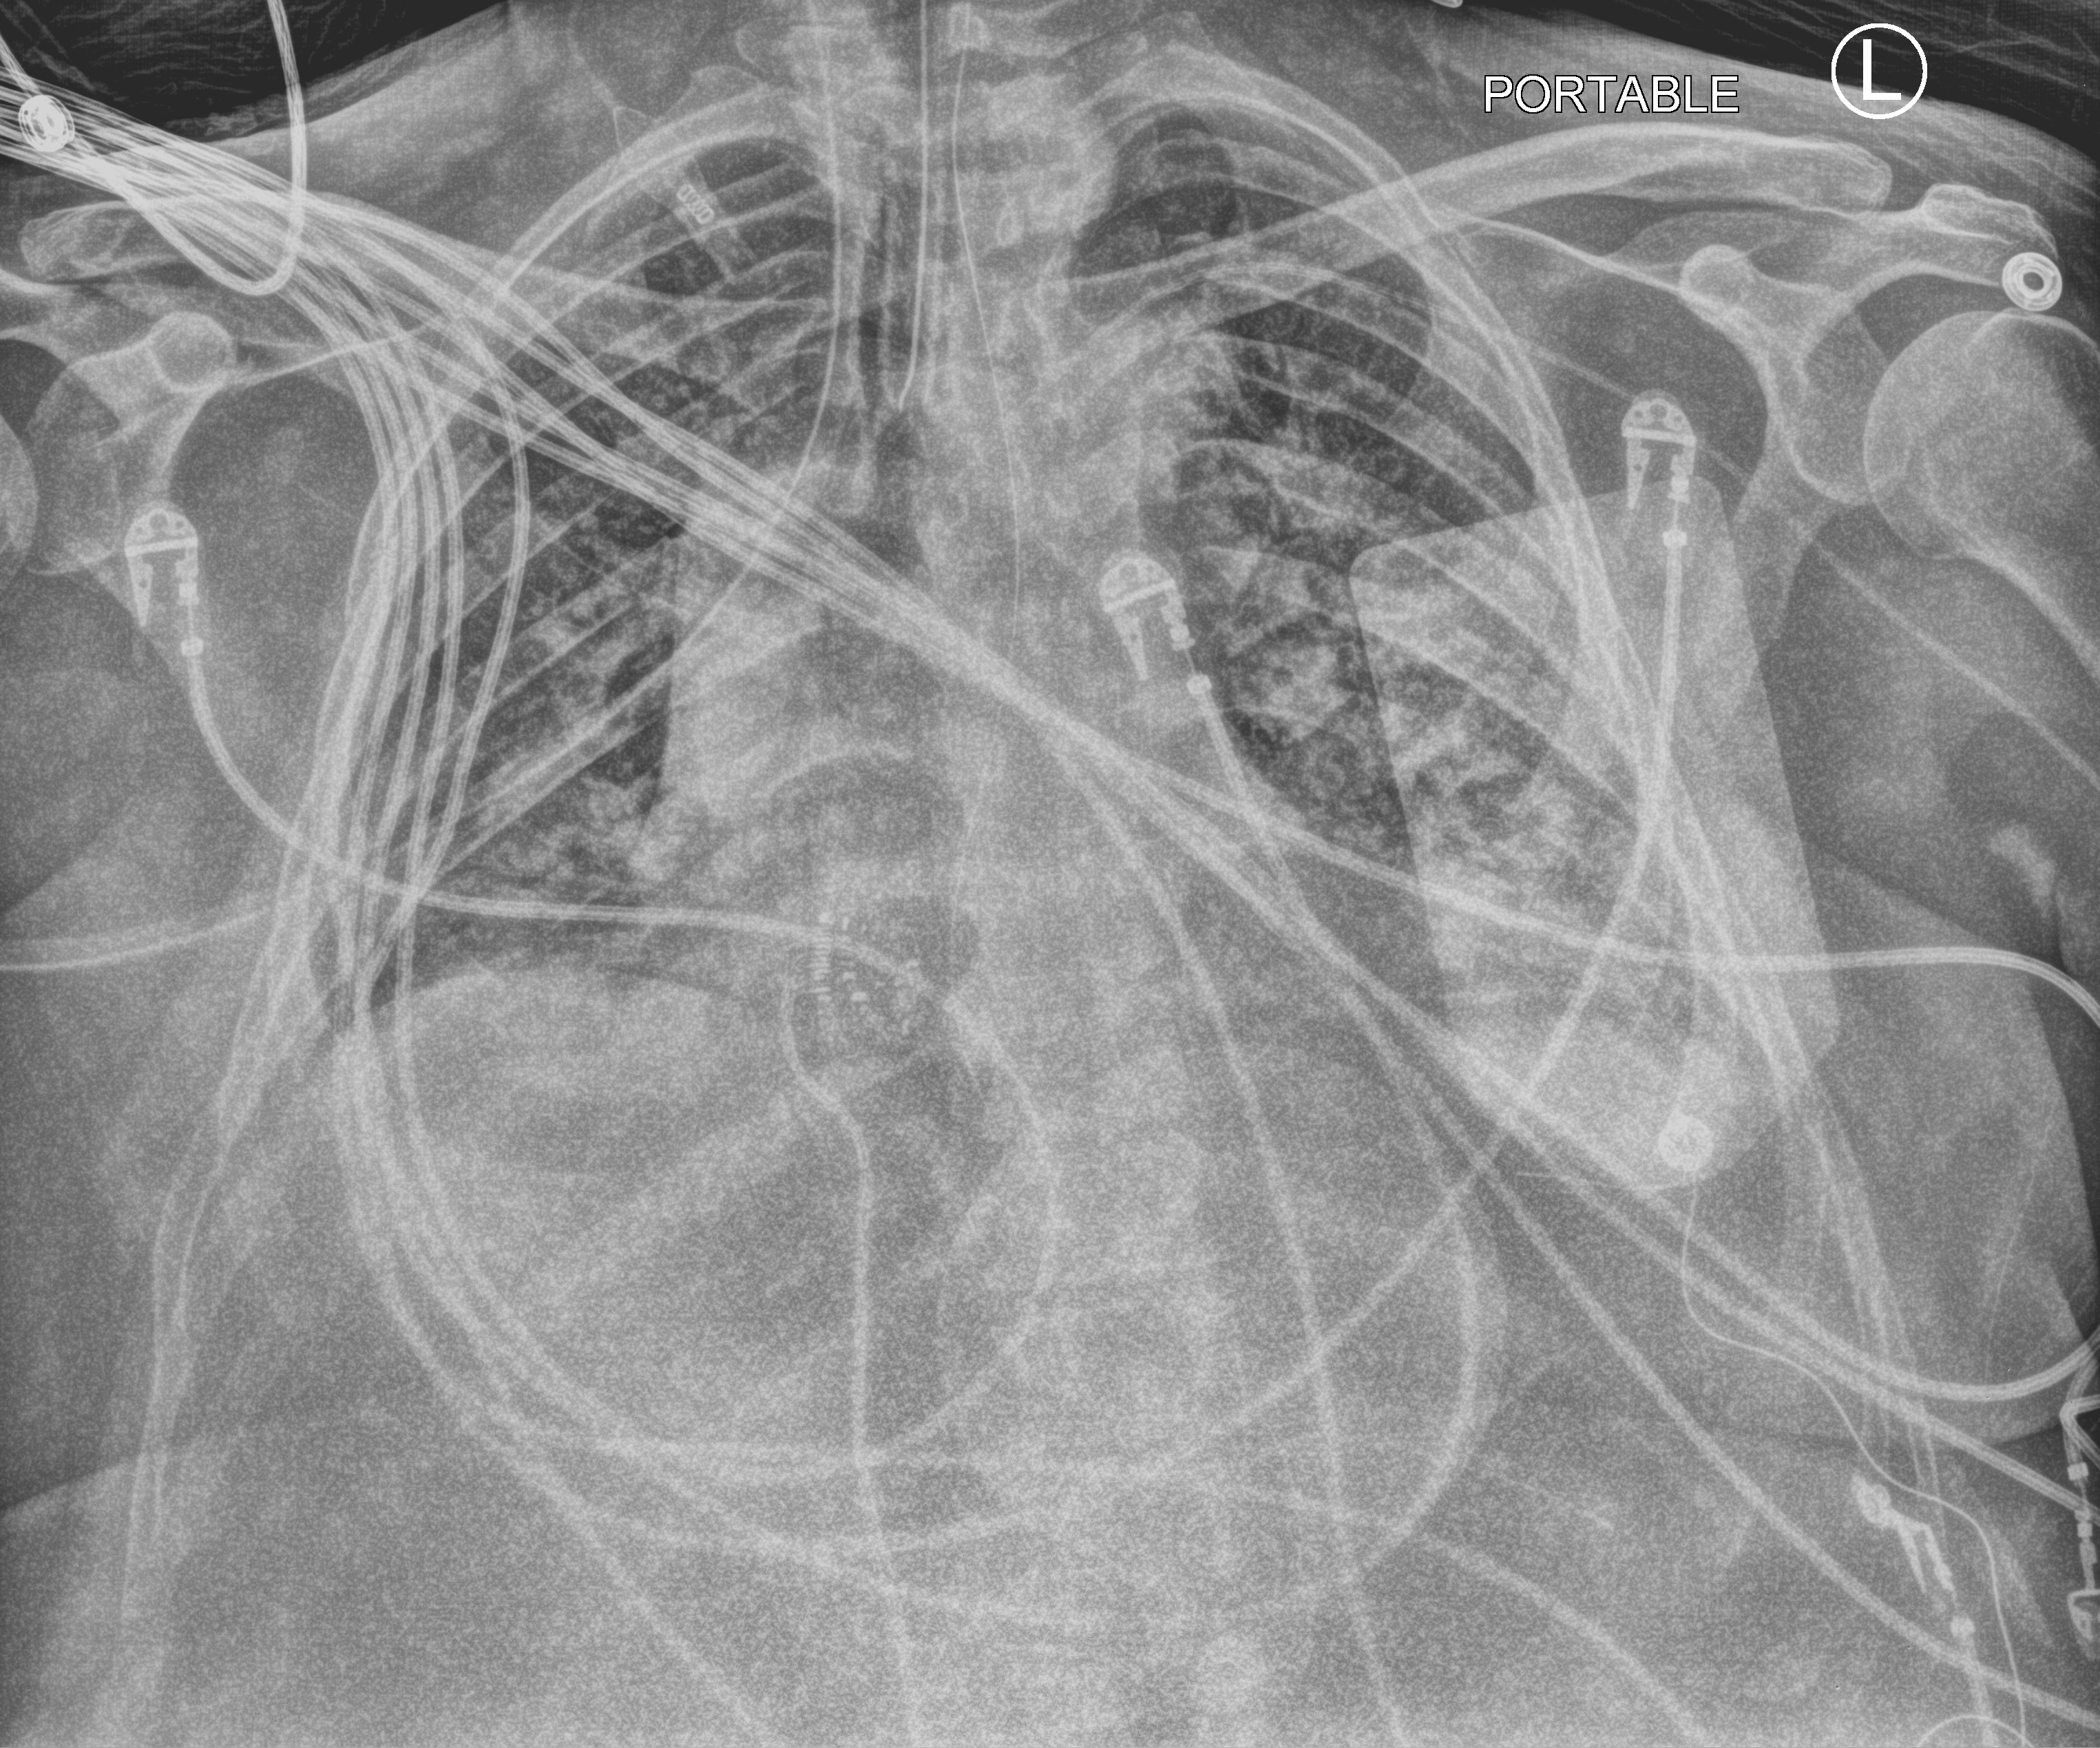
Chest X-ray (portable), anteroposterior (AP) projection. Male patient hospitalised with COVID-19, age 18–59 years.
From the hospital-stay record, not from the radiograph (when in the stay this image was taken is not recorded):
- length of hospital stay: 39 days
- admitted to intensive care during this hospital stay: yes